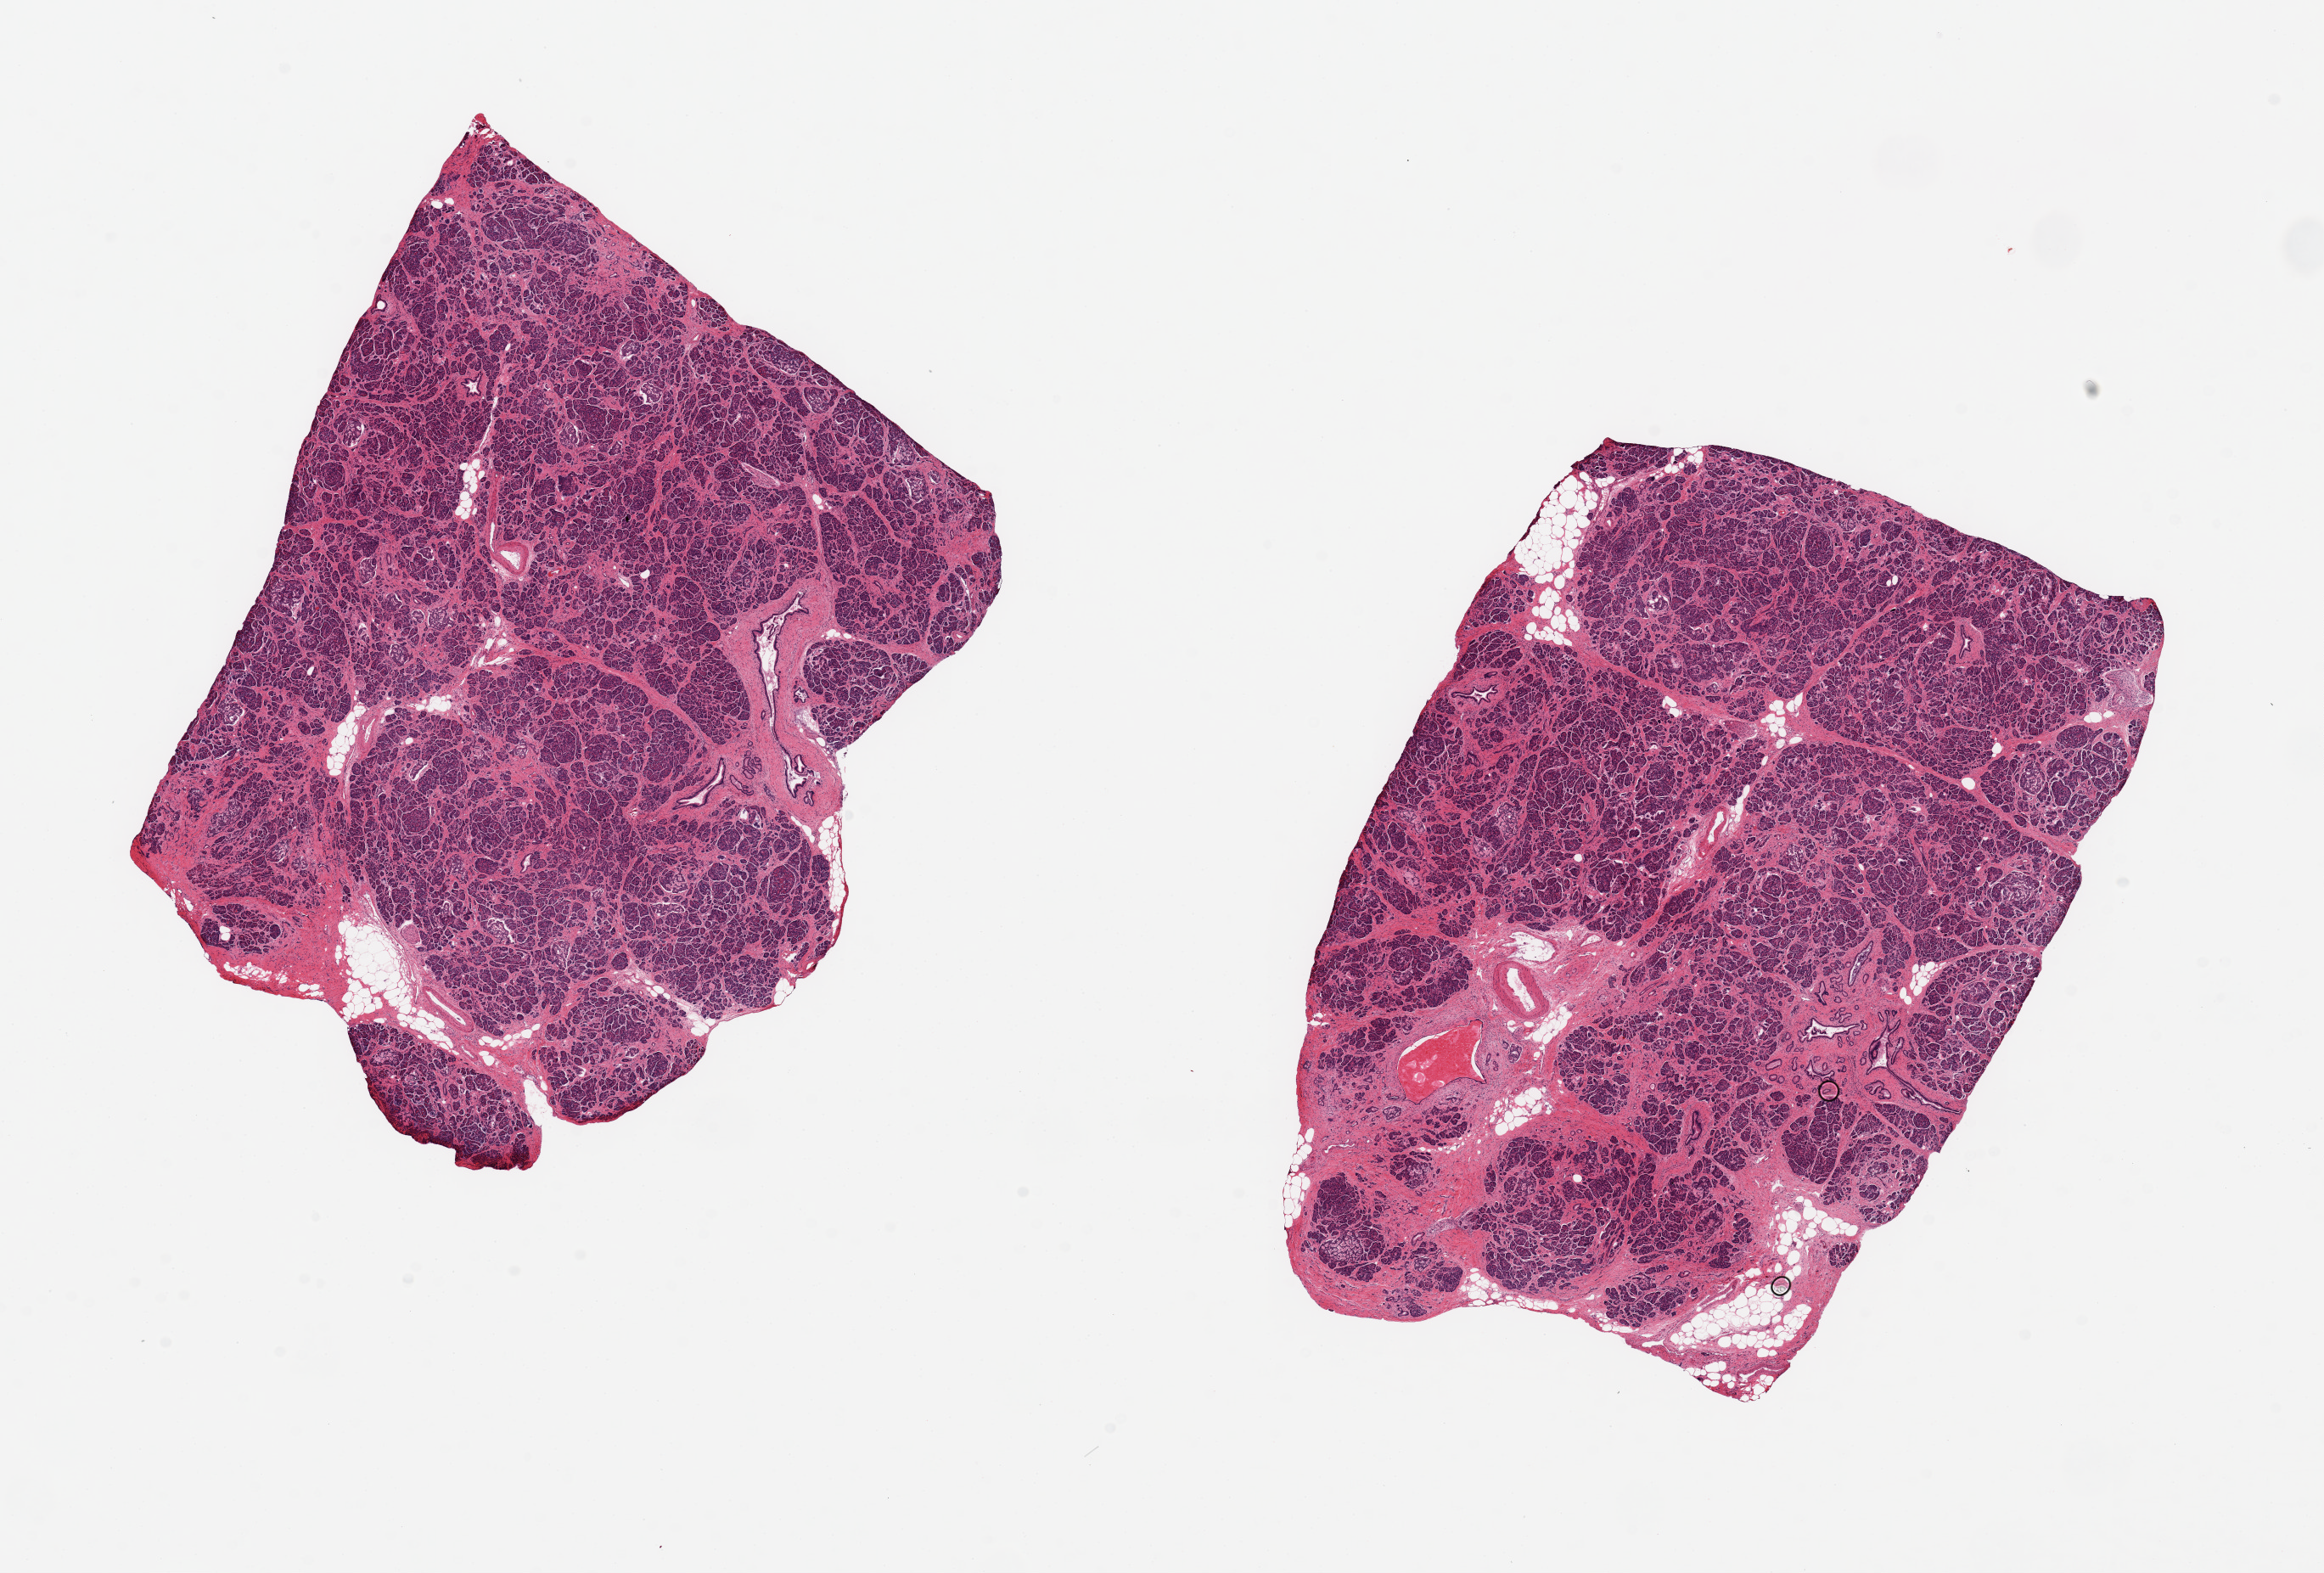
Digitized H&E-stained section, low-resolution overview of the scanned area, about 21.7 x 14.7 mm (from a 20x scan), PAXgene-fixed, paraffin-embedded tissue, target tissue: pancreas, tissue donor sample. Donor: male.
Pathologist's review note for this sample: 2 pieces ~8x6mm, interstitial fibrosis; Rare Islets seen; Fairly well preserved.